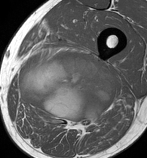
MRI of an extremity soft-tissue mass, one axial slice. Slice 60 of 86 in the series (ordered by position). MR volume resampled by the dataset authors to the PET/CT grid (not the native acquisition matrix). 3.27 mm slice thickness. 147 × 158 image matrix. Male patient. Case-level facts recorded for this patient, not image findings: histological type: undifferentiated pleomorphic liposarcoma; grade: high; site of the primary tumour: left thigh.
Annotated regions visible in this slice (expert contour drawn on MRI and transferred to this co-registered scan by the dataset authors):
- gross tumour volume including surrounding oedema: bounding box <18,51,116,130> (left, top, right, bottom; pixels)
- gross tumour volume (mass): <19,51,116,123>